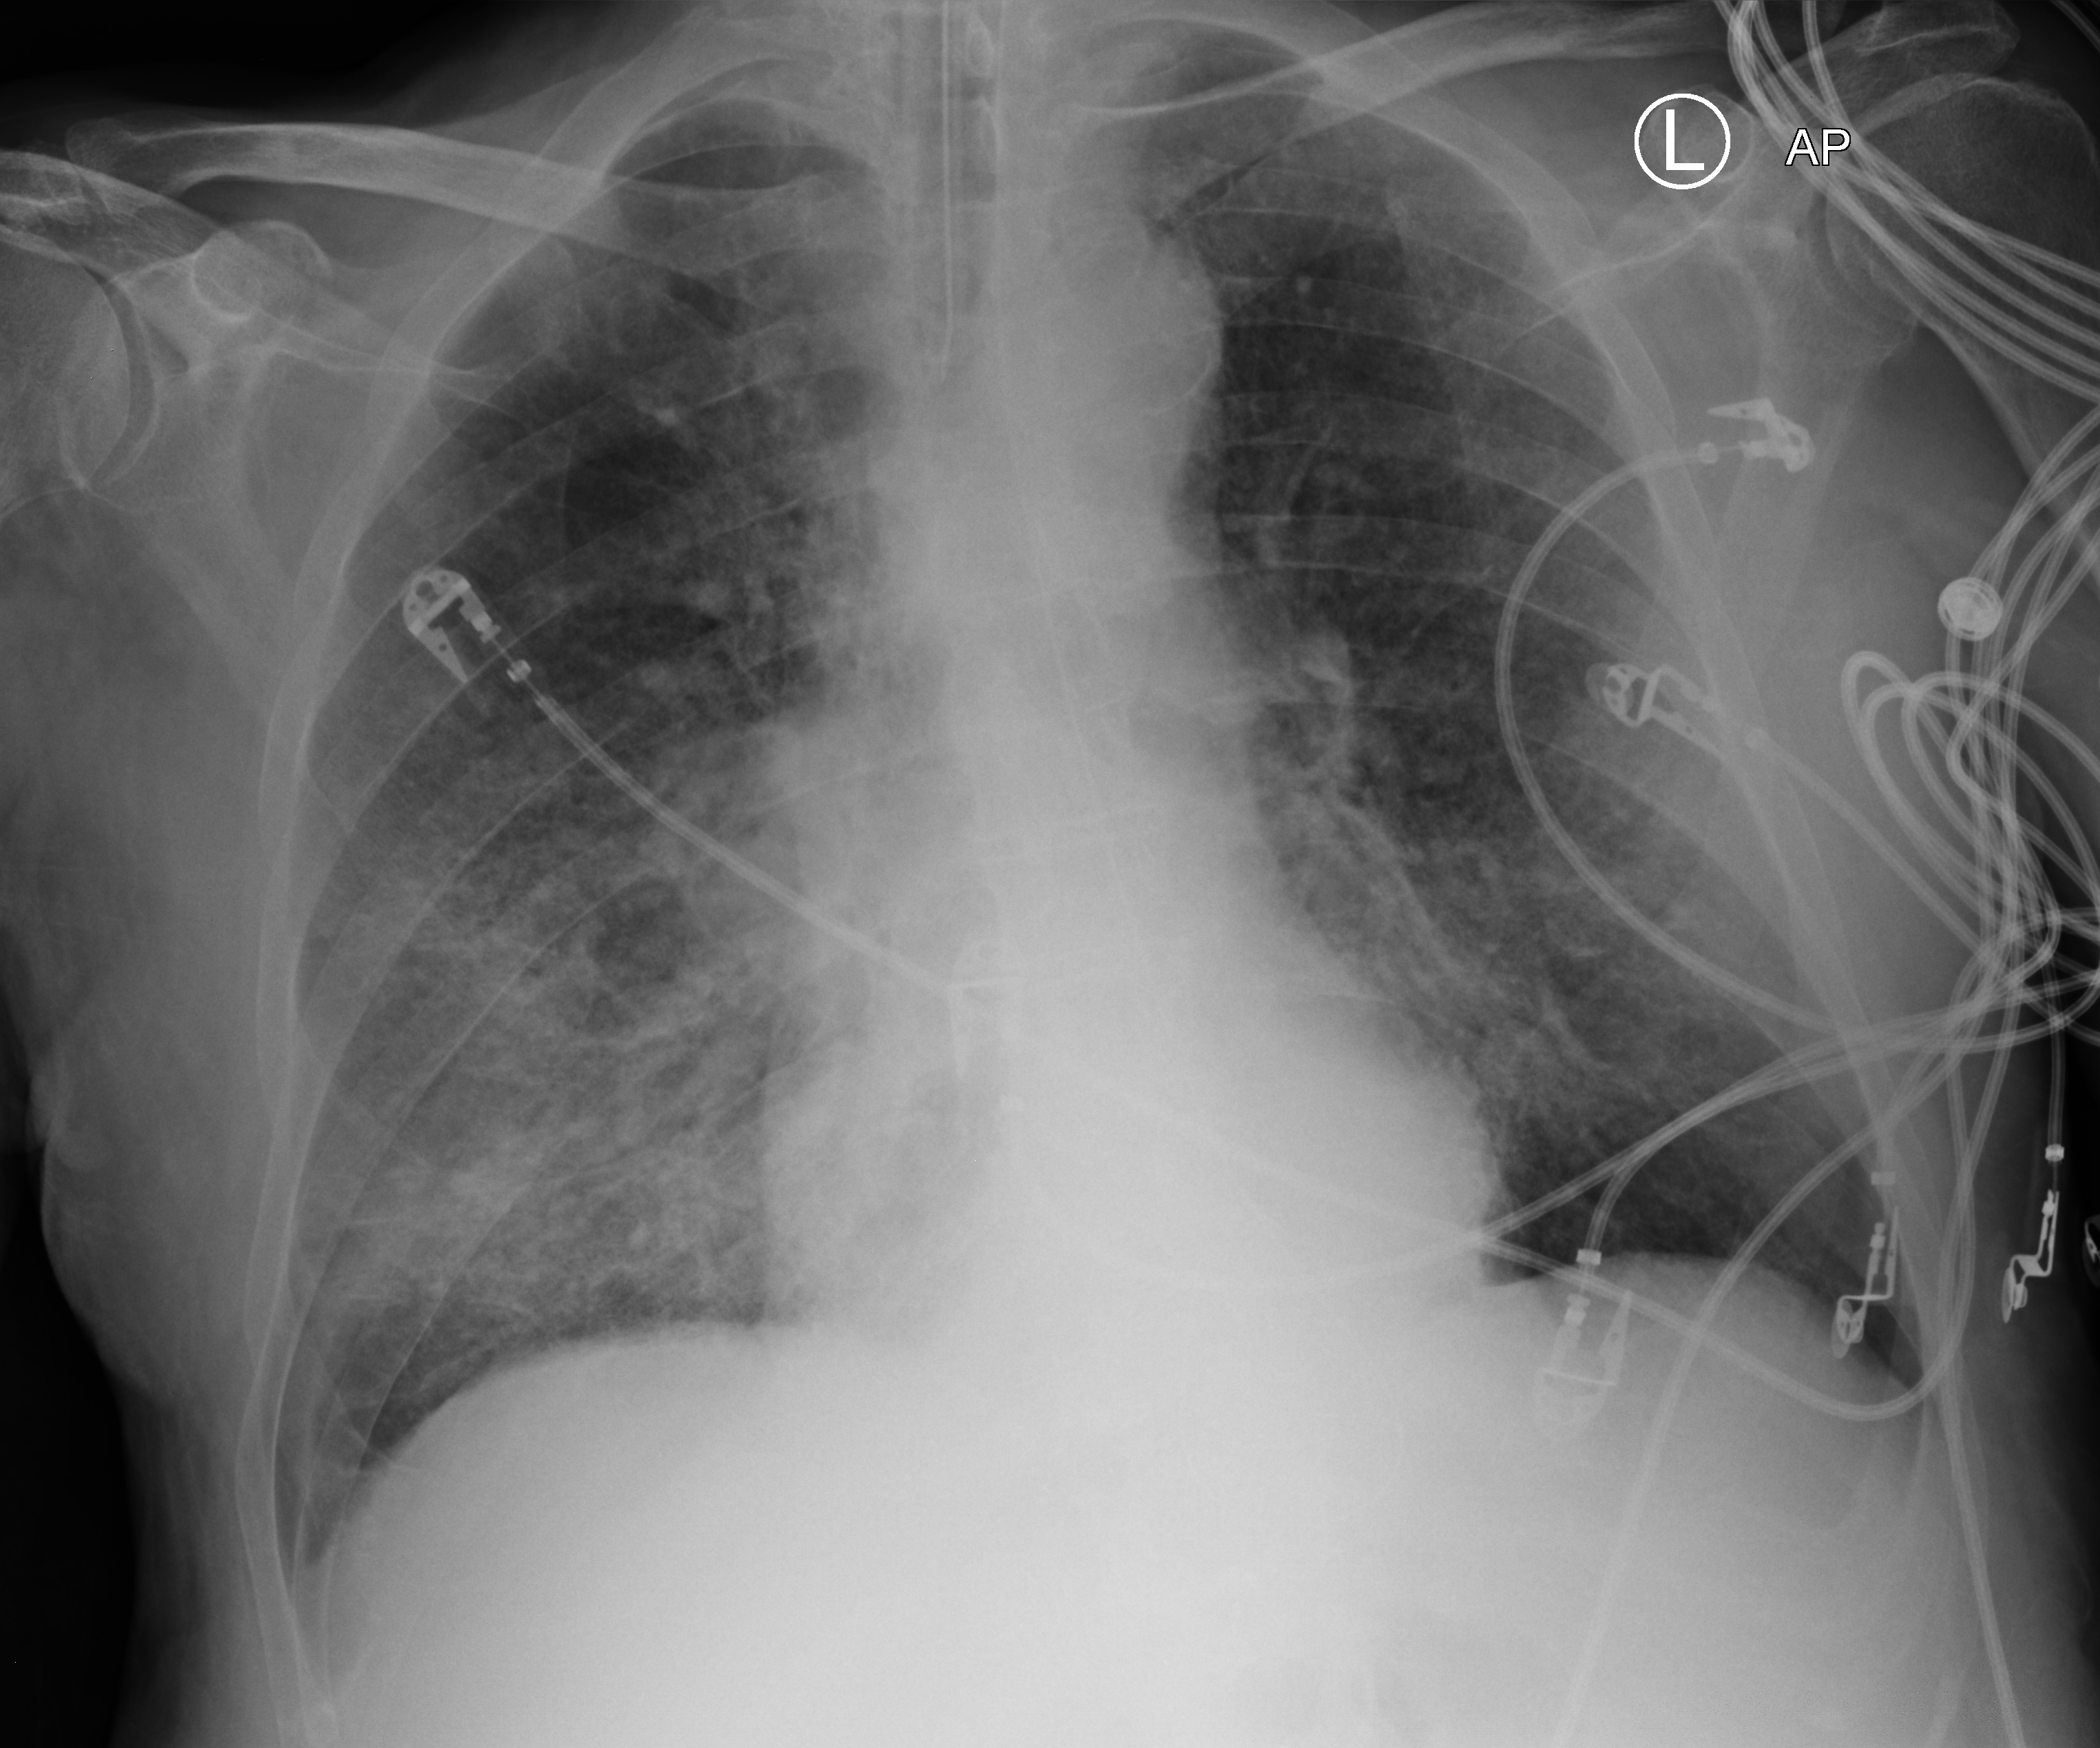
Chest X-ray (portable), anteroposterior (AP) projection. Male patient hospitalised with COVID-19, age 75–90 years.
Admission-level facts for this patient (not findings on this image; timing relative to this image not recorded): admitted to intensive care during this hospital stay: yes; smoking status (admission record): former; mechanically ventilated during this hospital stay: yes.